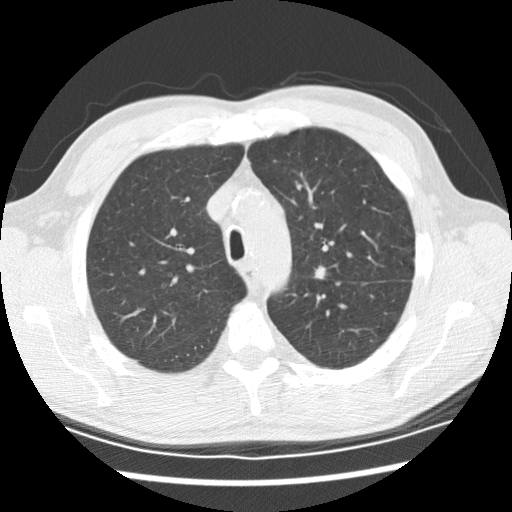
Low-dose screening chest CT, one axial slice; position 153 of 208 along the scan axis; reconstruction kernel STANDARD; lung window (W 1500 / L -600 HU); 512 × 512 image matrix.
Outlined on this slice (outlined manually by an expert reader):
- lesion 1 (tumor, upper lobe of left lung): bounding box [x1, y1, x2, y2] px = [315, 266, 326, 280]